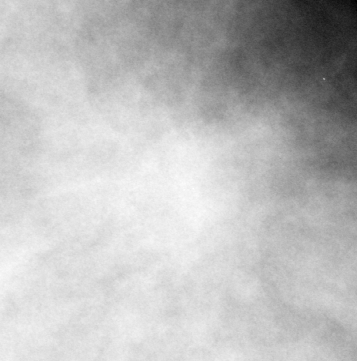
Cropped region of a digitized screen-film mammogram centred on a radiologist-marked abnormality; left breast; CC view.
Marked abnormality: mass, shape irregular, margins spiculated; BI-RADS assessment category 5; subtlety rating 4 on a 1 (subtle) to 5 (obvious) scale; pathology result (as recorded, not read from the image): malignant.